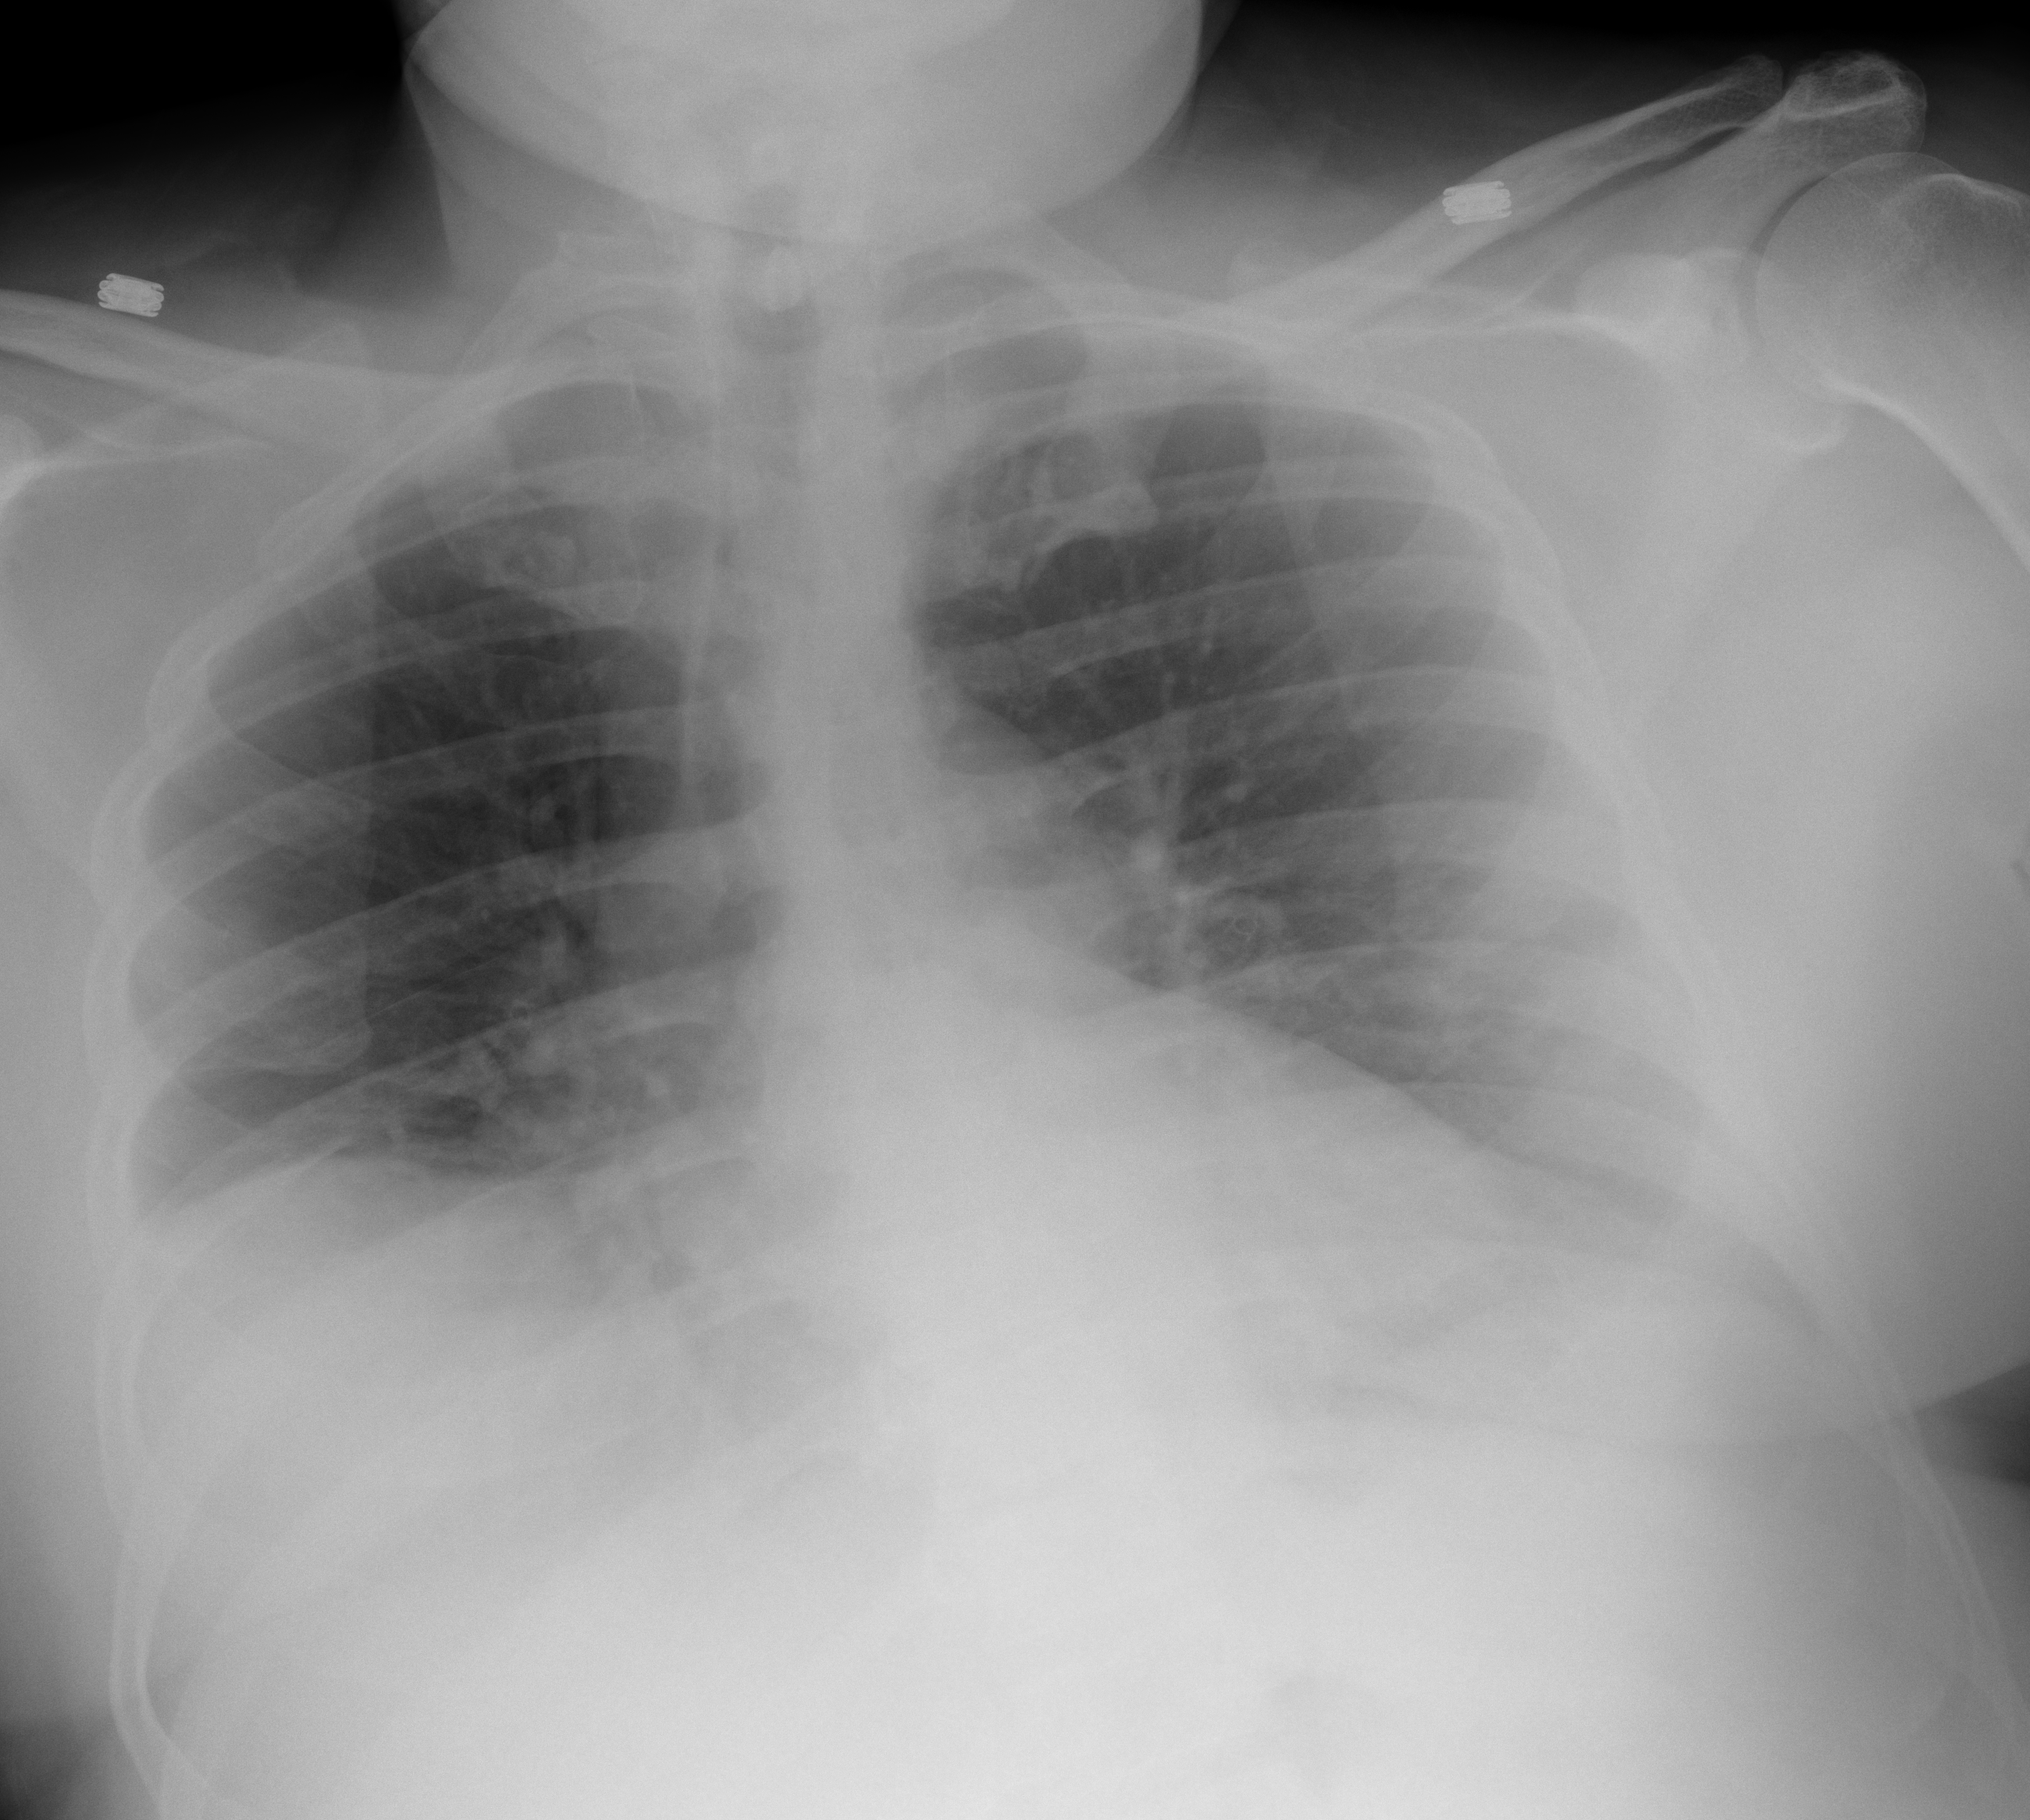
Portable chest radiograph, AP projection. Male patient, age 63 years; imaged 0 days after the COVID-19 diagnosis.
Key findings recorded by the radiologist: interval development of right pleural effusion with bibasilar linear opacity.